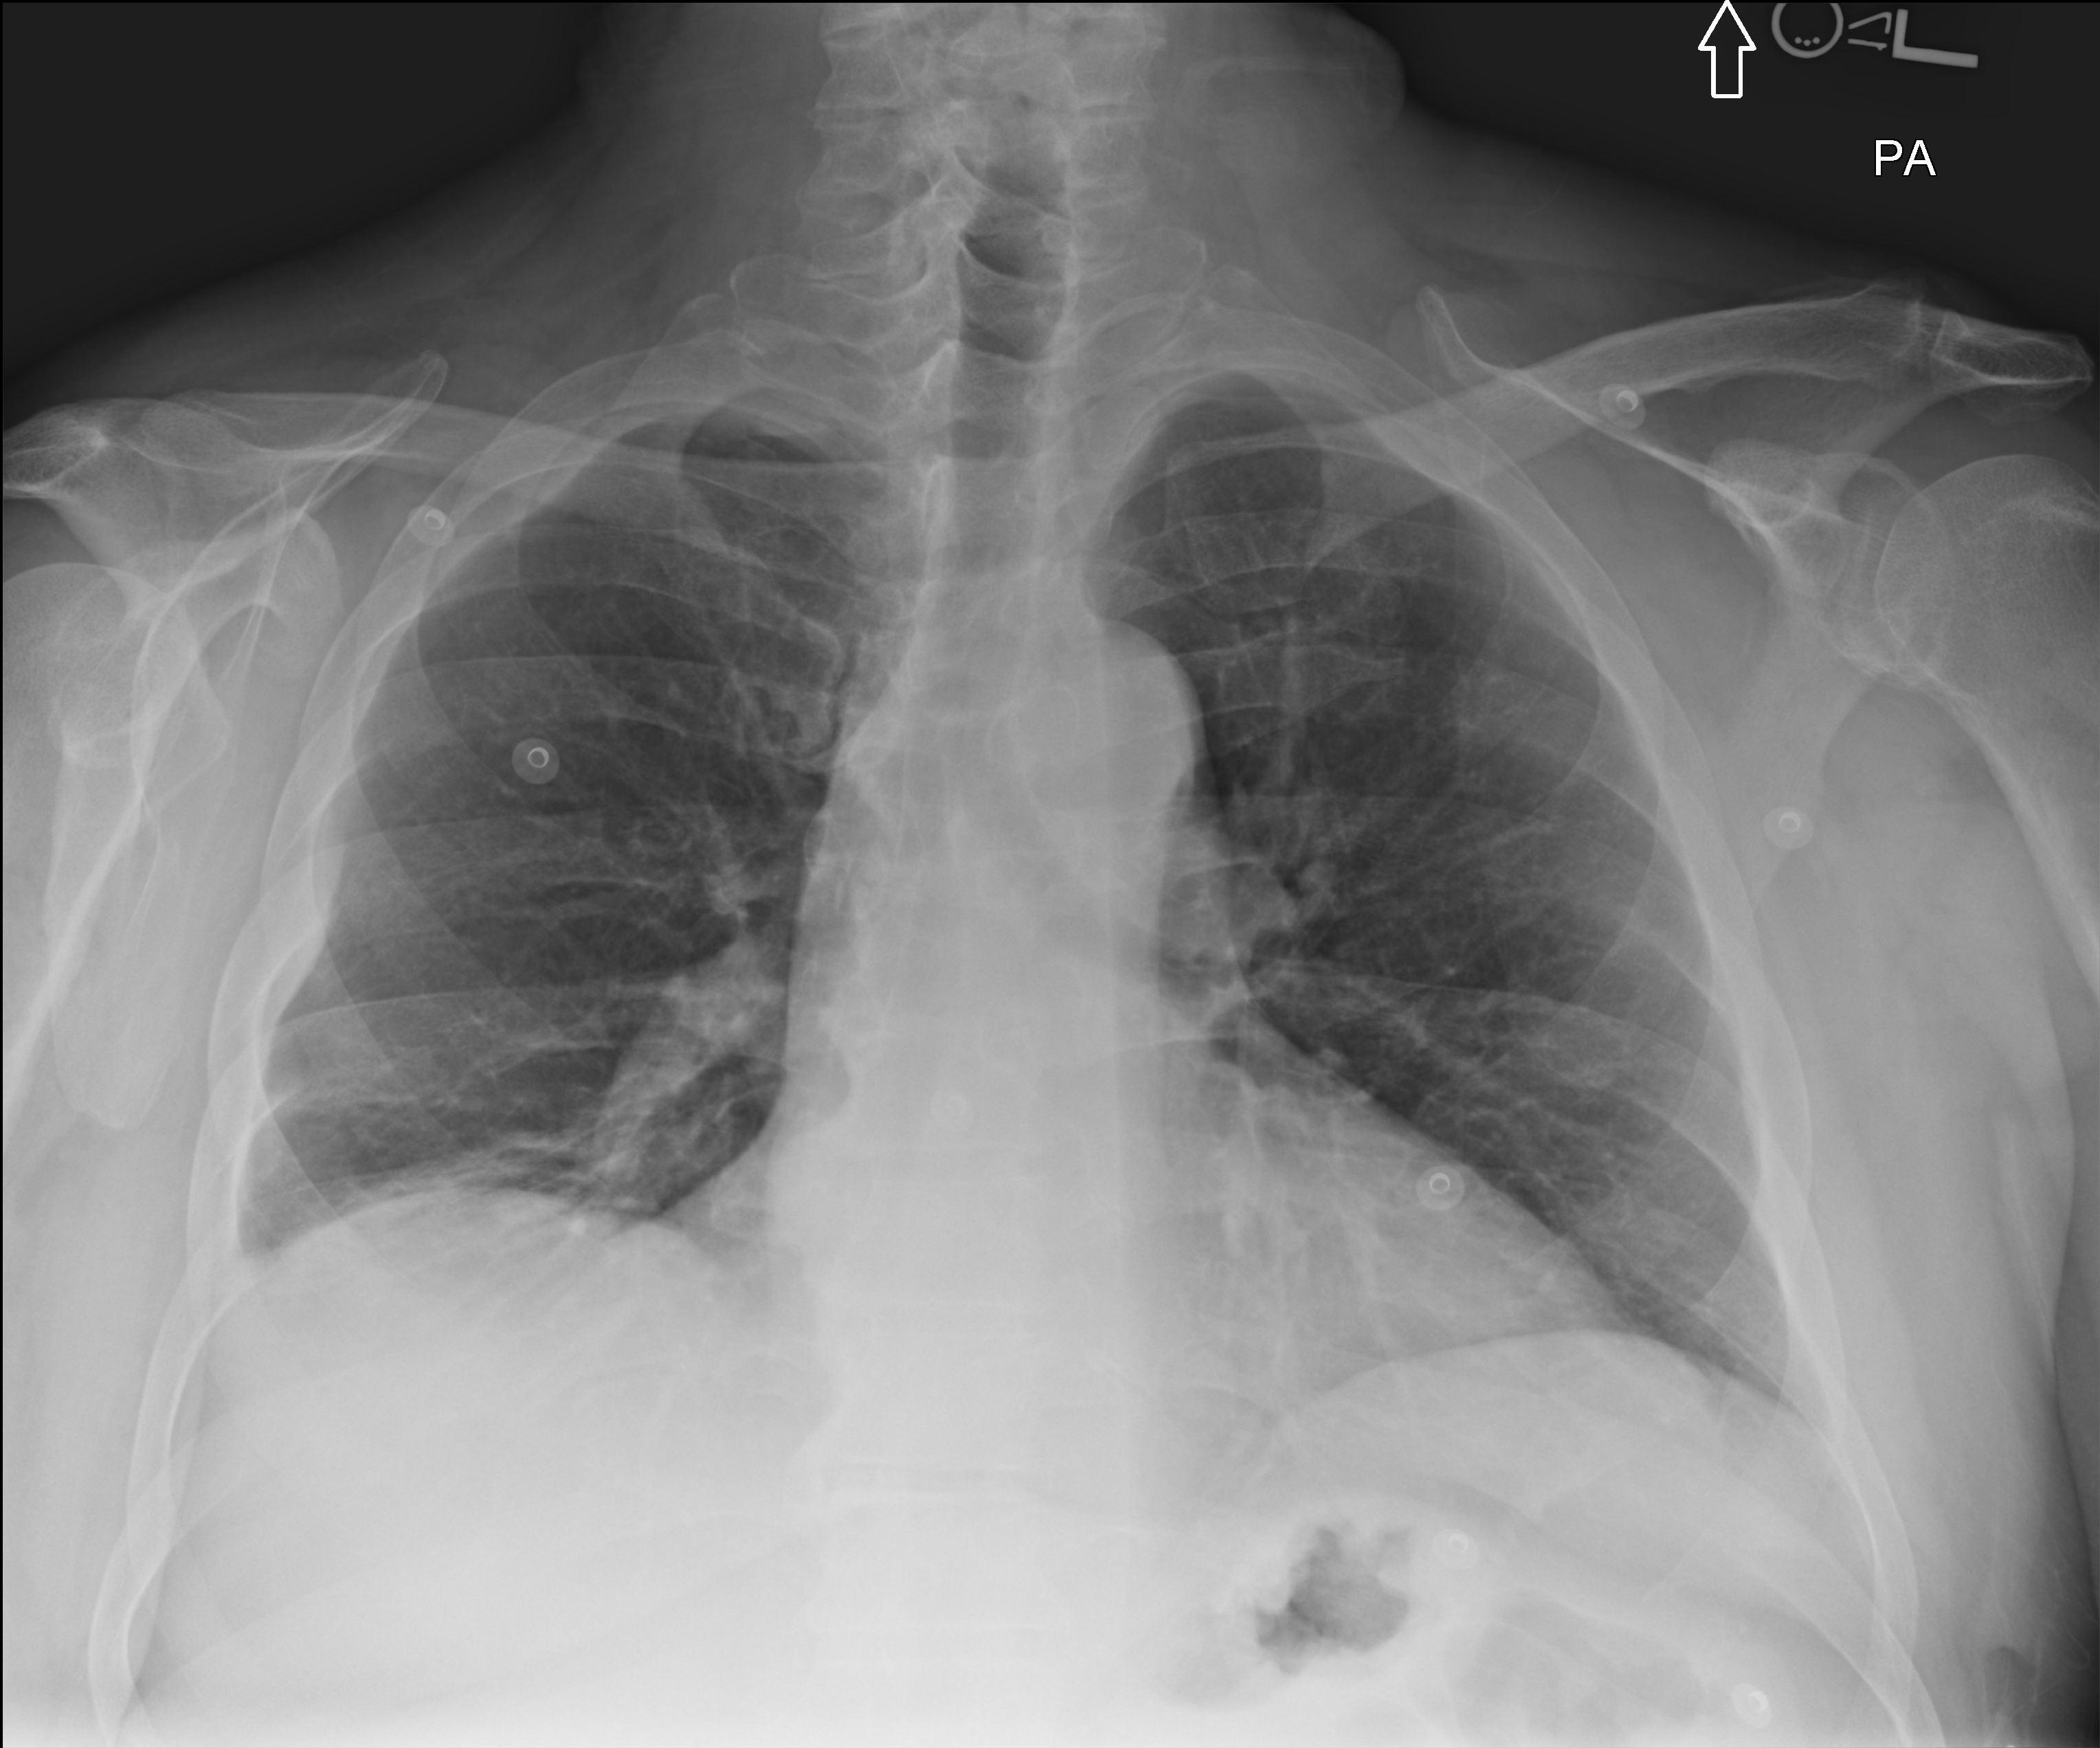
Chest X-ray; posteroanterior (PA) projection. Male patient hospitalised with COVID-19, age 60–74 years.
Admission-level facts for this patient (not findings on this image; timing relative to this image not recorded): mechanically ventilated during this hospital stay: no.